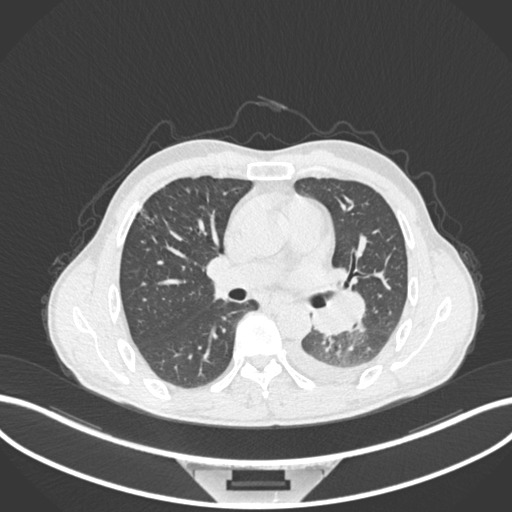
Chest CT, one axial slice. Slice 136 of 222 in the series (ordered by position). Reconstruction kernel B30f. 120 kVp. Lung window (W 1500 / L -600 HU). 512 × 512 image matrix, field of view 400 × 400 mm. Male patient, age 47 years. From the clinical record (not read from this slice): clinical TNM (as recorded): T3 N1 M1c; histopathological grade: G3.
Structures marked on this image (bounding box drawn by a radiologist):
- lung tumour (recorded histology: small cell carcinoma): box from (x=307, y=286) to (x=369, y=336) px